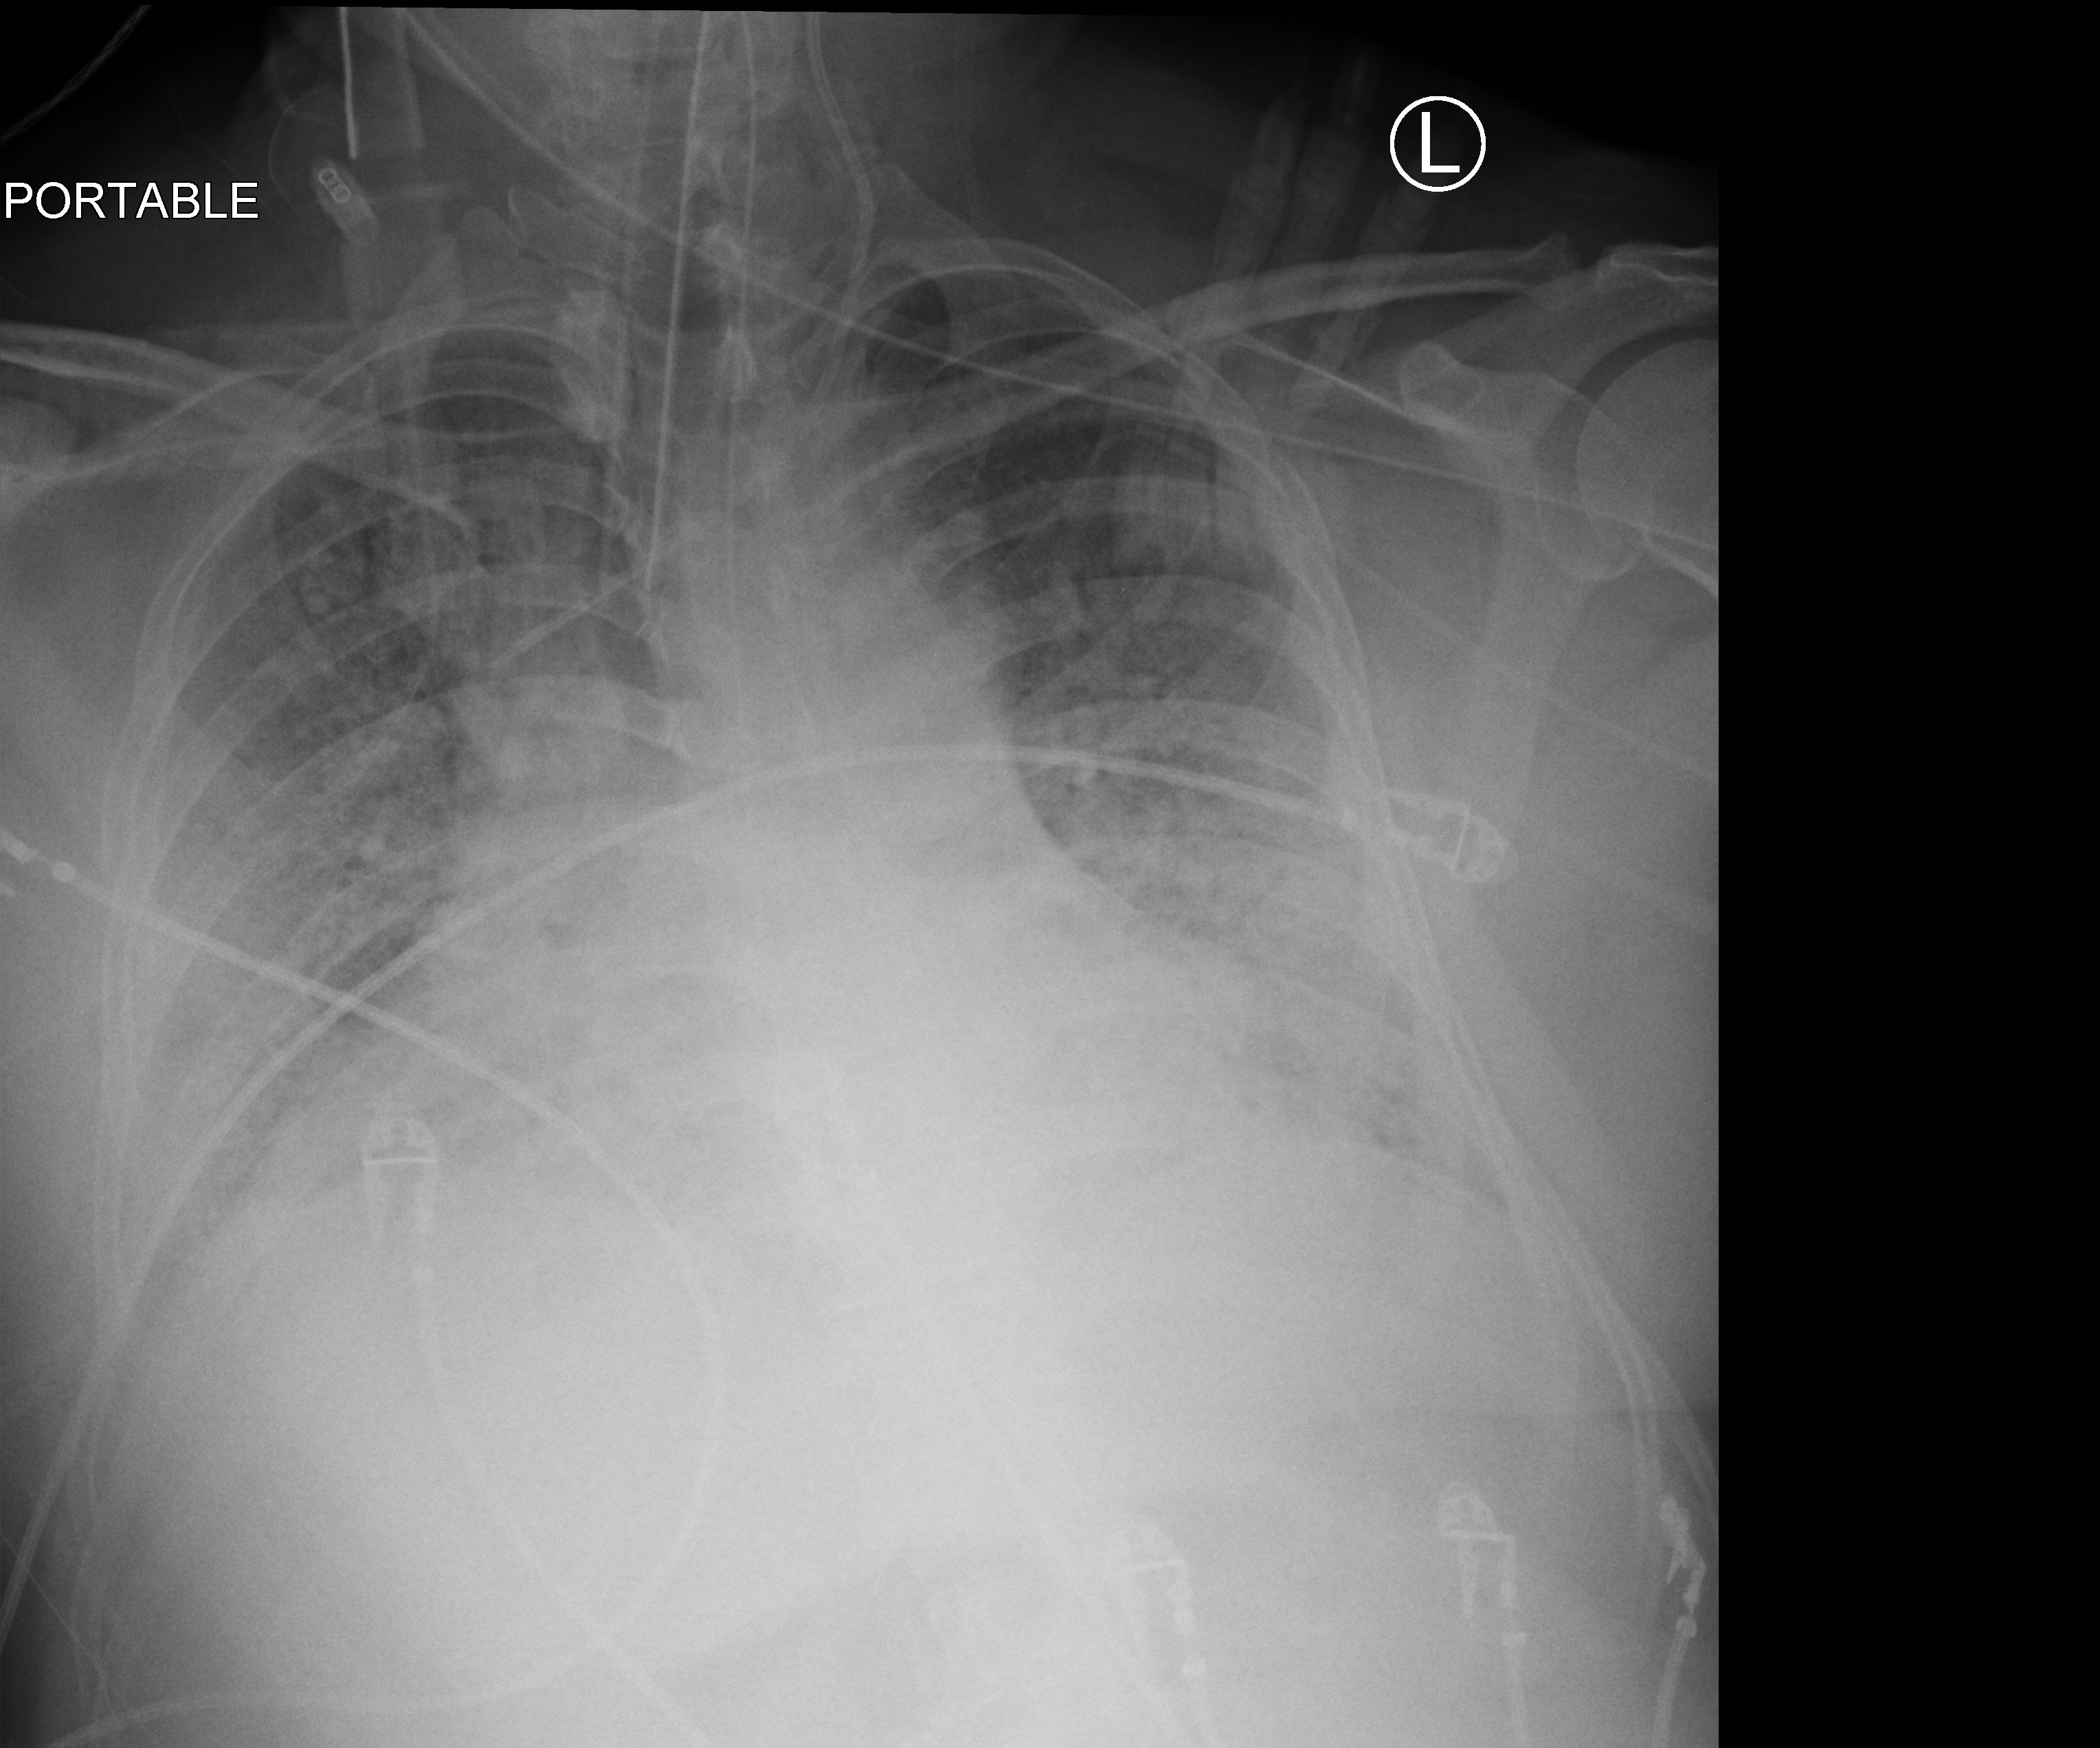
Chest X-ray (portable); anteroposterior (AP) projection. Adult patient hospitalised with COVID-19, age 18–59 years.
Hospital-stay facts (about this admission, not read from this image; timing relative to this image not recorded): smoking status (admission record): never; admitted to intensive care during this hospital stay: yes.